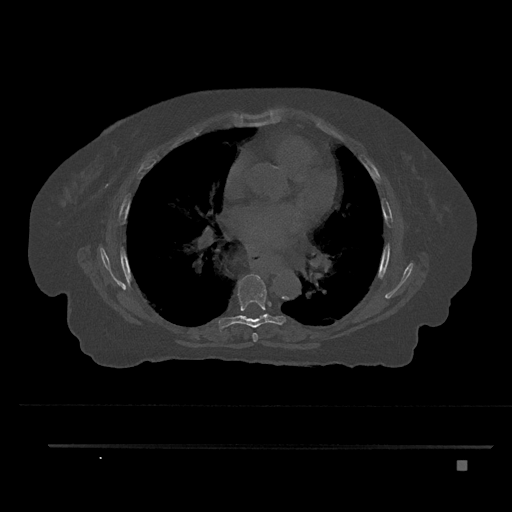
CT including the spine, one axial slice. Slice 490 of 797 in the series (ordered by position). Bone window (W 1800 / L 400 HU). 0.5 mm slice thickness. 512 × 512 image matrix, field of view 437 × 437 mm. Female patient, age 76 years. Case-level facts recorded for this patient, not image findings: primary cancer: lung; vertebrae with lytic lesions (as recorded): T11, L3.
Outlined on this slice (semi-automatic segmentation, software-assisted and operator-edited):
- T6 vertebra: bounding box (x1, y1, x2, y2) in pixels: (252, 333, 258, 342)
- T7 vertebra: (219, 274, 286, 331)
- T8 vertebra: (242, 315, 261, 318)